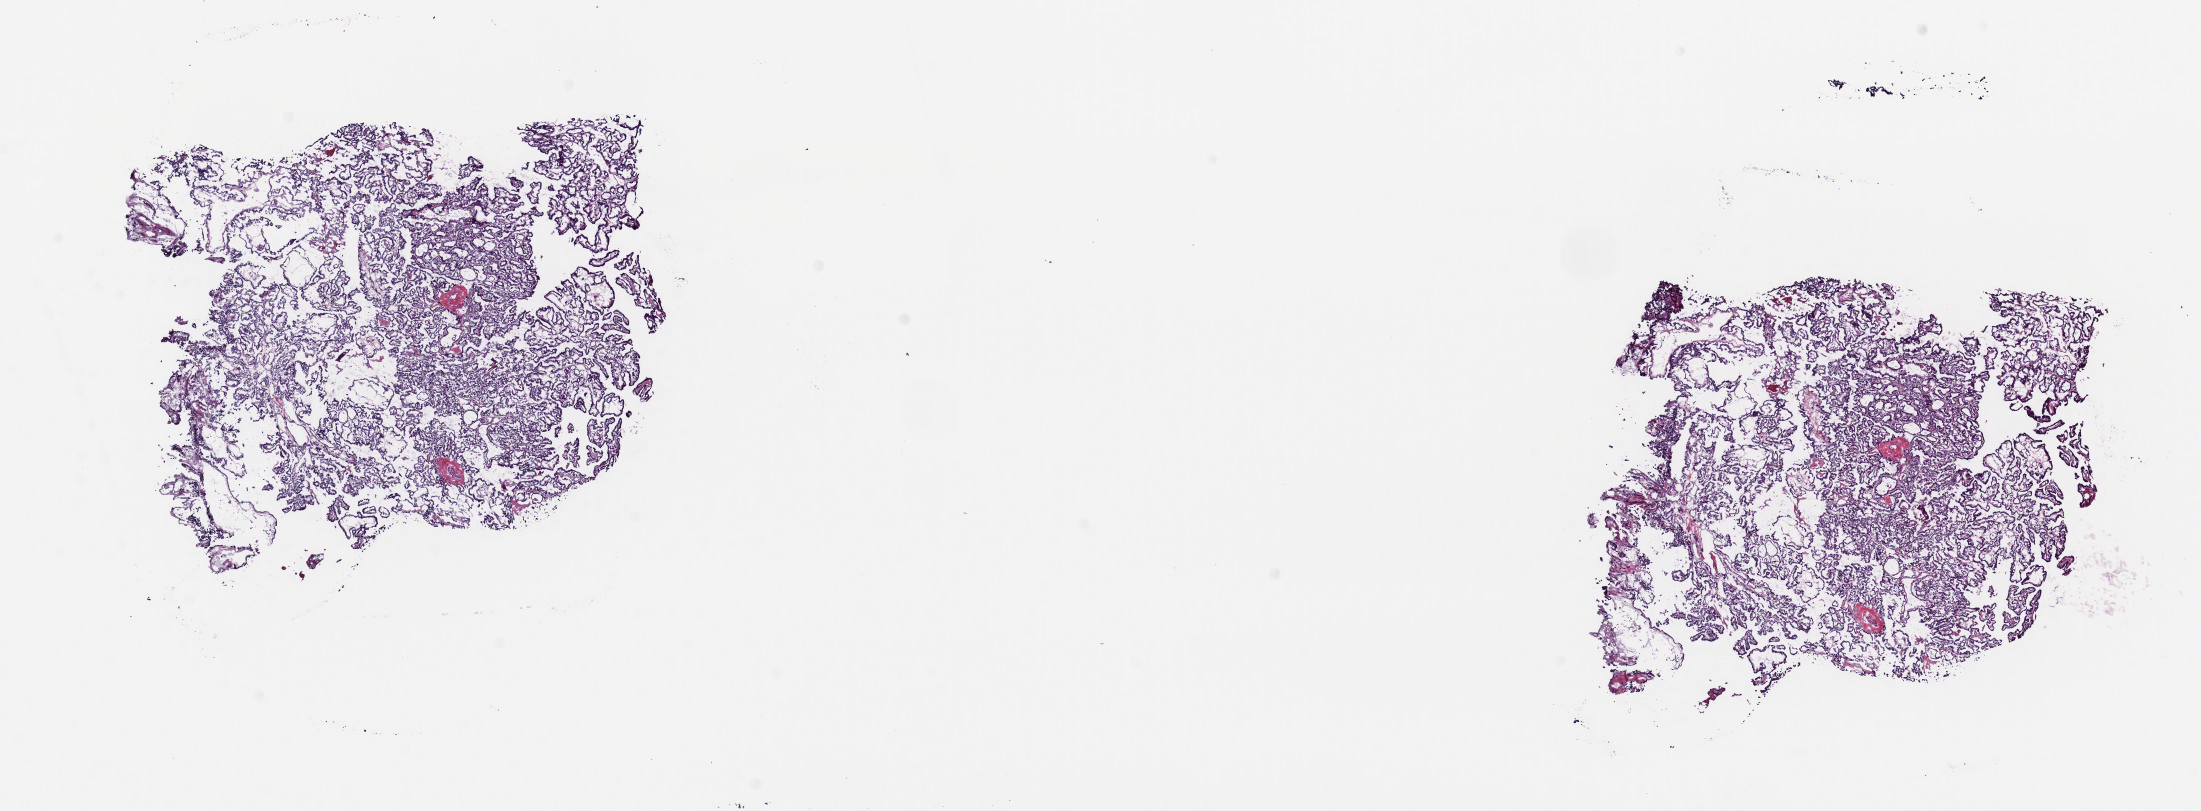
Whole-slide histology image, H&E-stained — shown as a low-resolution overview of the whole scanned area (about 17.4 x 6.4 mm, from a 40x scan); frozen section from the top of the tissue portion; thyroid, primary tumour sample. Patient: female, age at initial diagnosis 37 years. Slide review estimates, as recorded: tumour cells 90%, tumour nuclei 100%, normal cells 0%, stromal cells 10%, necrosis 0%. Inflammatory infiltration, as recorded: lymphocyte infiltration 1%, monocyte infiltration 1%, neutrophil infiltration 0%.
• TNM: T3 N1 MX
• AJCC pathologic stage: I (6th edition)
• laterality: left
• diagnosis: Papillary adenocarcinoma, NOS (thyroid gland)